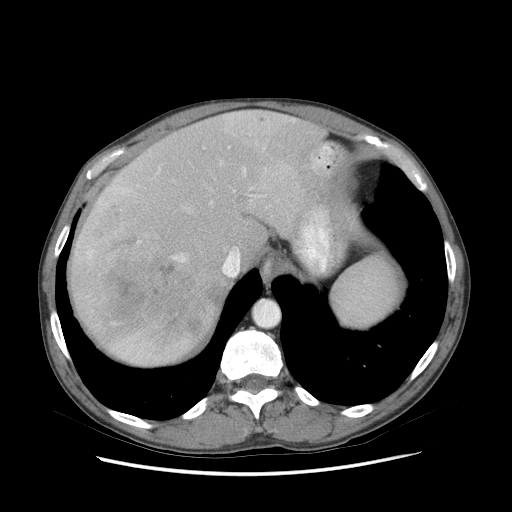
Contrast-enhanced abdominal CT (liver protocol), one axial slice; slice 63 of 89 in the series (ordered by position); soft-tissue window (W 400 / L 40 HU); 2.5 mm slice thickness; 512 × 512 image matrix, field of view 380 × 380 mm. From the clinical record (not read from this slice): diagnosis: hepatocellular carcinoma (patient treated with transarterial chemoembolisation; whether this scan precedes or follows treatment is not stated here); TNM stage (as recorded): Stage-IIIB; Child-Pugh class: A.
Outlined on this slice (semi-automatically segmented with operator editing):
- liver parenchyma outside the tumour (the mass and vessels are separate outlines, so this box may not span the whole liver): box from (x=70, y=110) to (x=342, y=364) px
- mass: (x=79, y=204)–(x=212, y=342)
- liver vessels: (x=78, y=146)–(x=331, y=357)